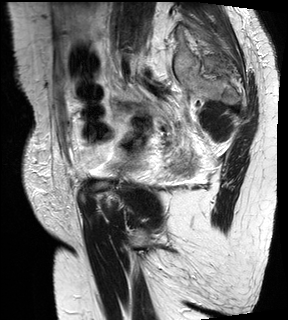
Pelvic MRI for cervical cancer, one sagittal slice. Slice 7 of 28 in the series (ordered by position). T2-weighted. 1.5 T. TE 89 ms, TR 2740 ms. 4 mm slice thickness. 288 × 320 image matrix. Female patient, age 59 years.
Outlined on this slice (expert manual segmentation):
- uterus and cervix: bounding box (x1, y1, x2, y2) in pixels: (173, 154, 193, 173)